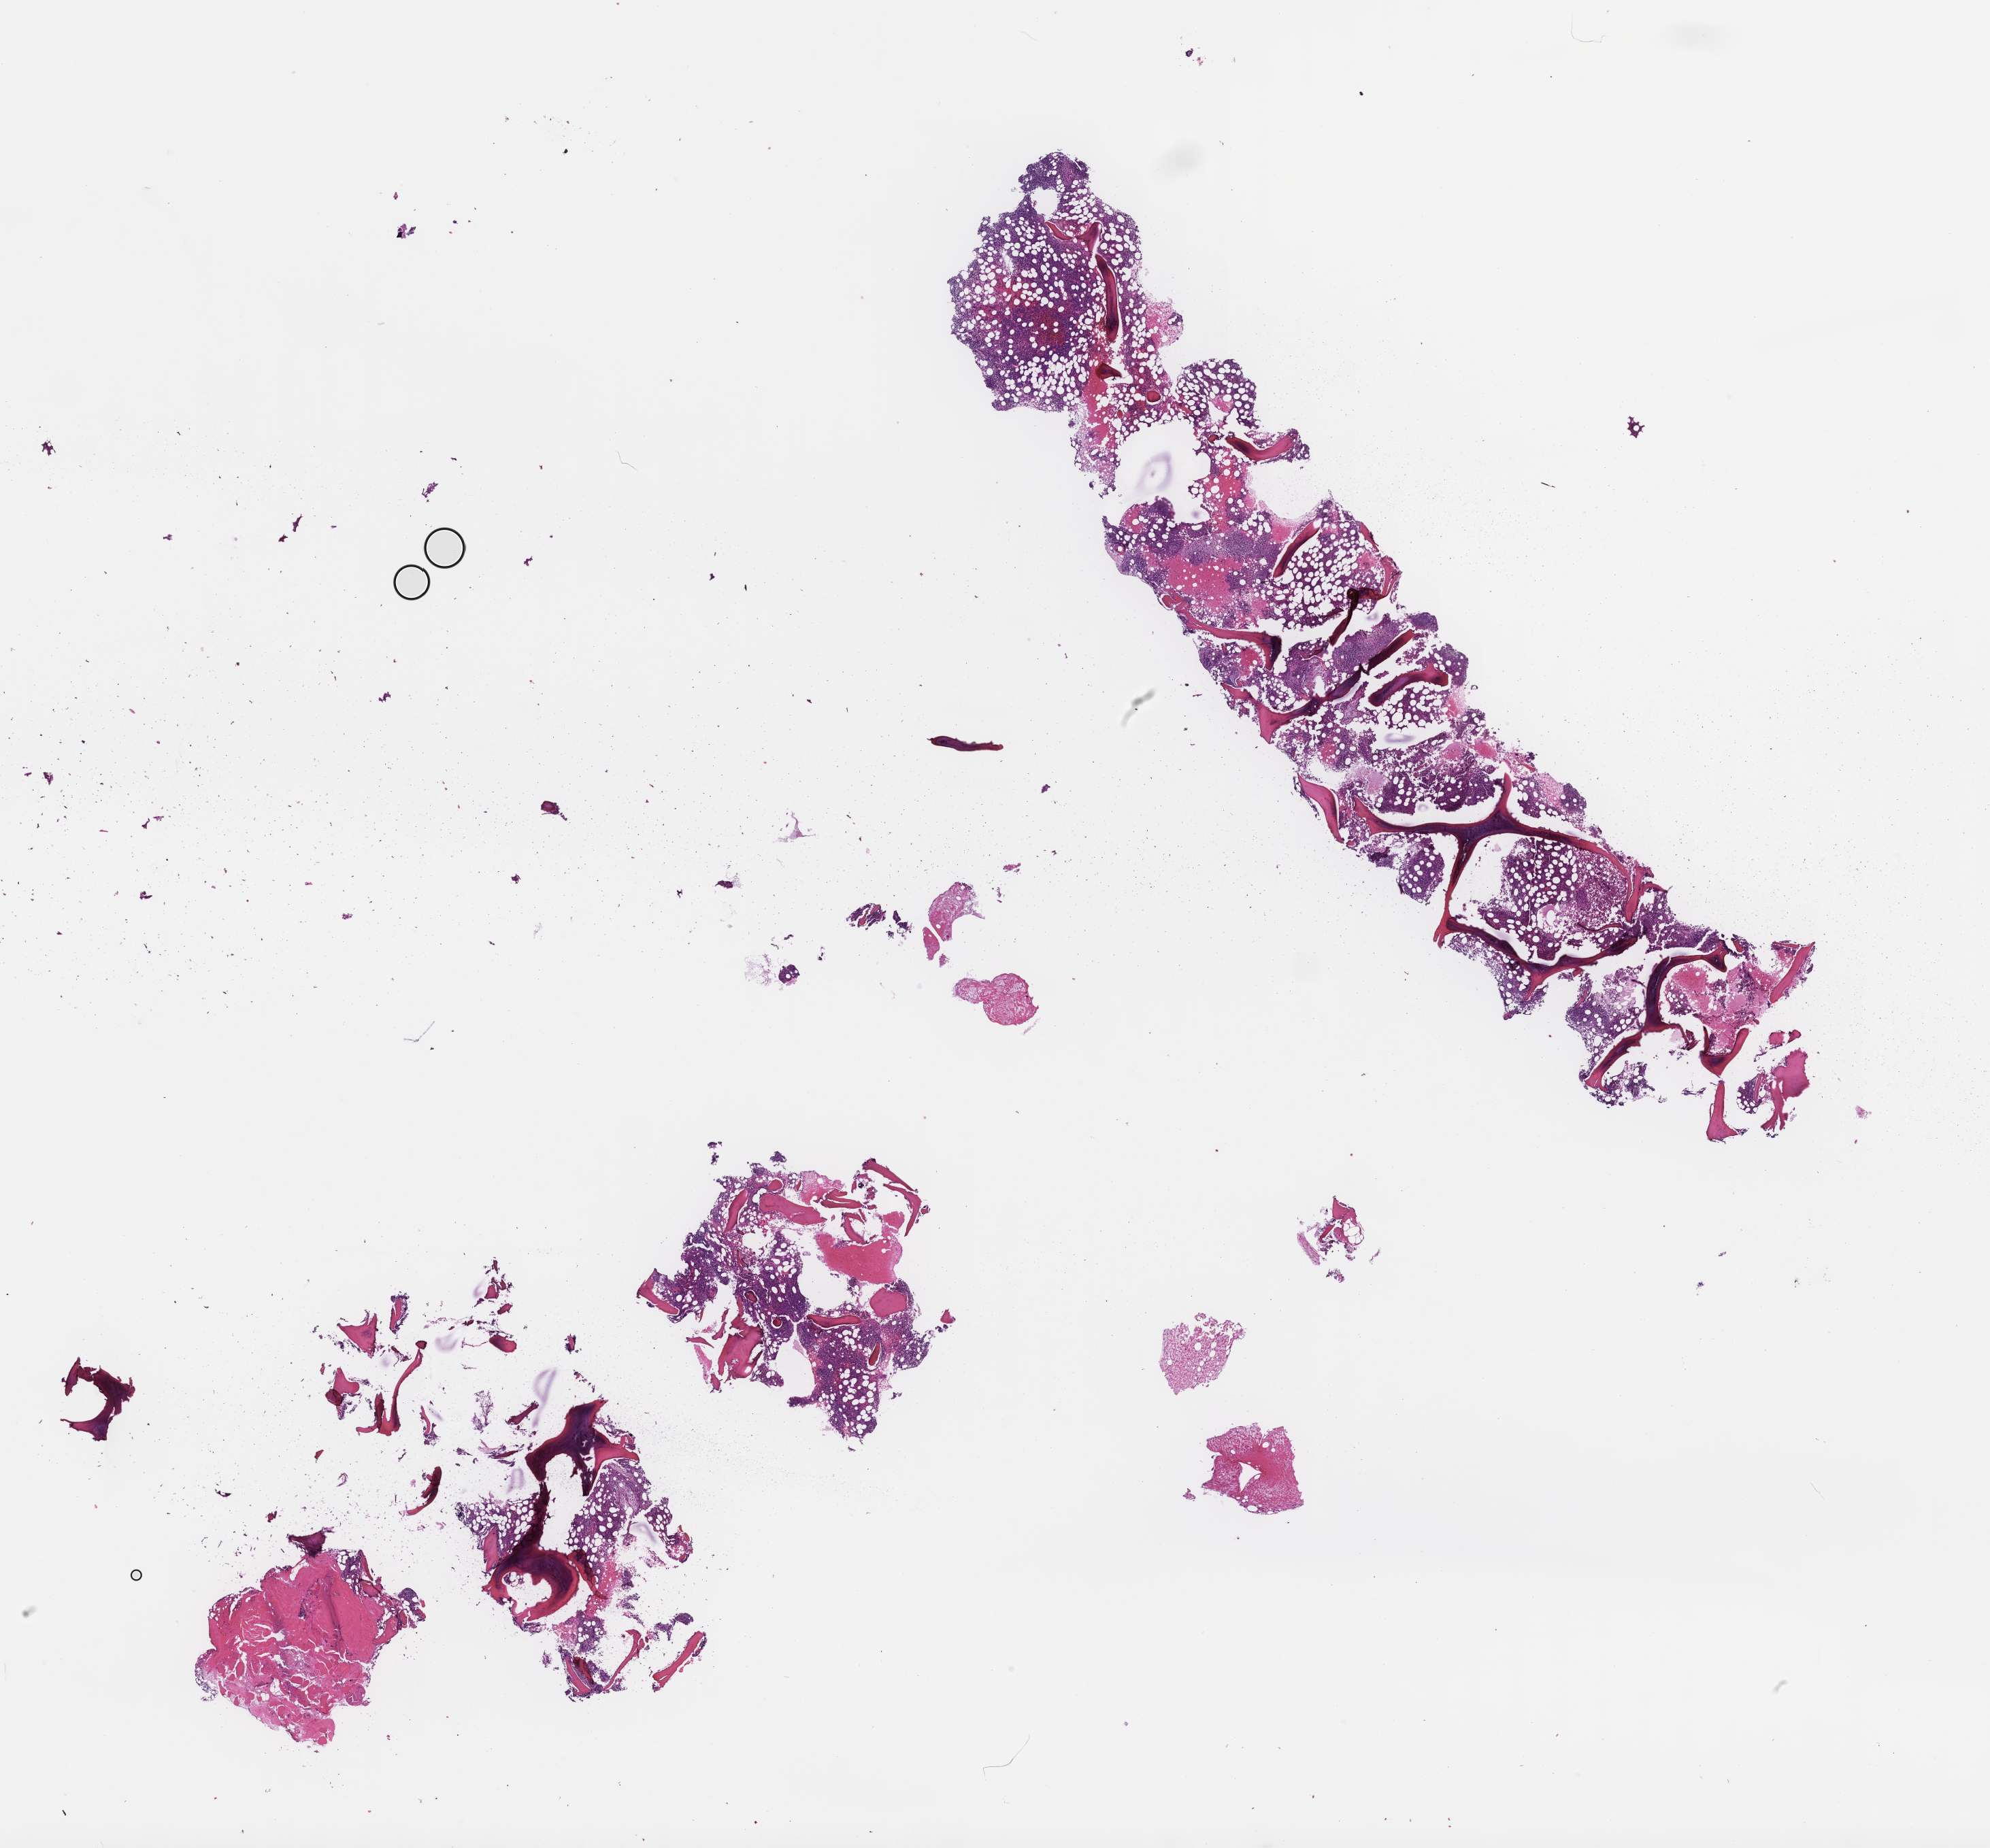
Whole-slide image, H&E stain, a low-resolution overview of the entire scanned area, about 23.6 x 21.9 mm; formalin-fixed paraffin-embedded section; tissue site: bone marrow; archival tissue. Male patient.
This section: primary tumour tissue. Diagnosis: Plasma Cell Myeloma.